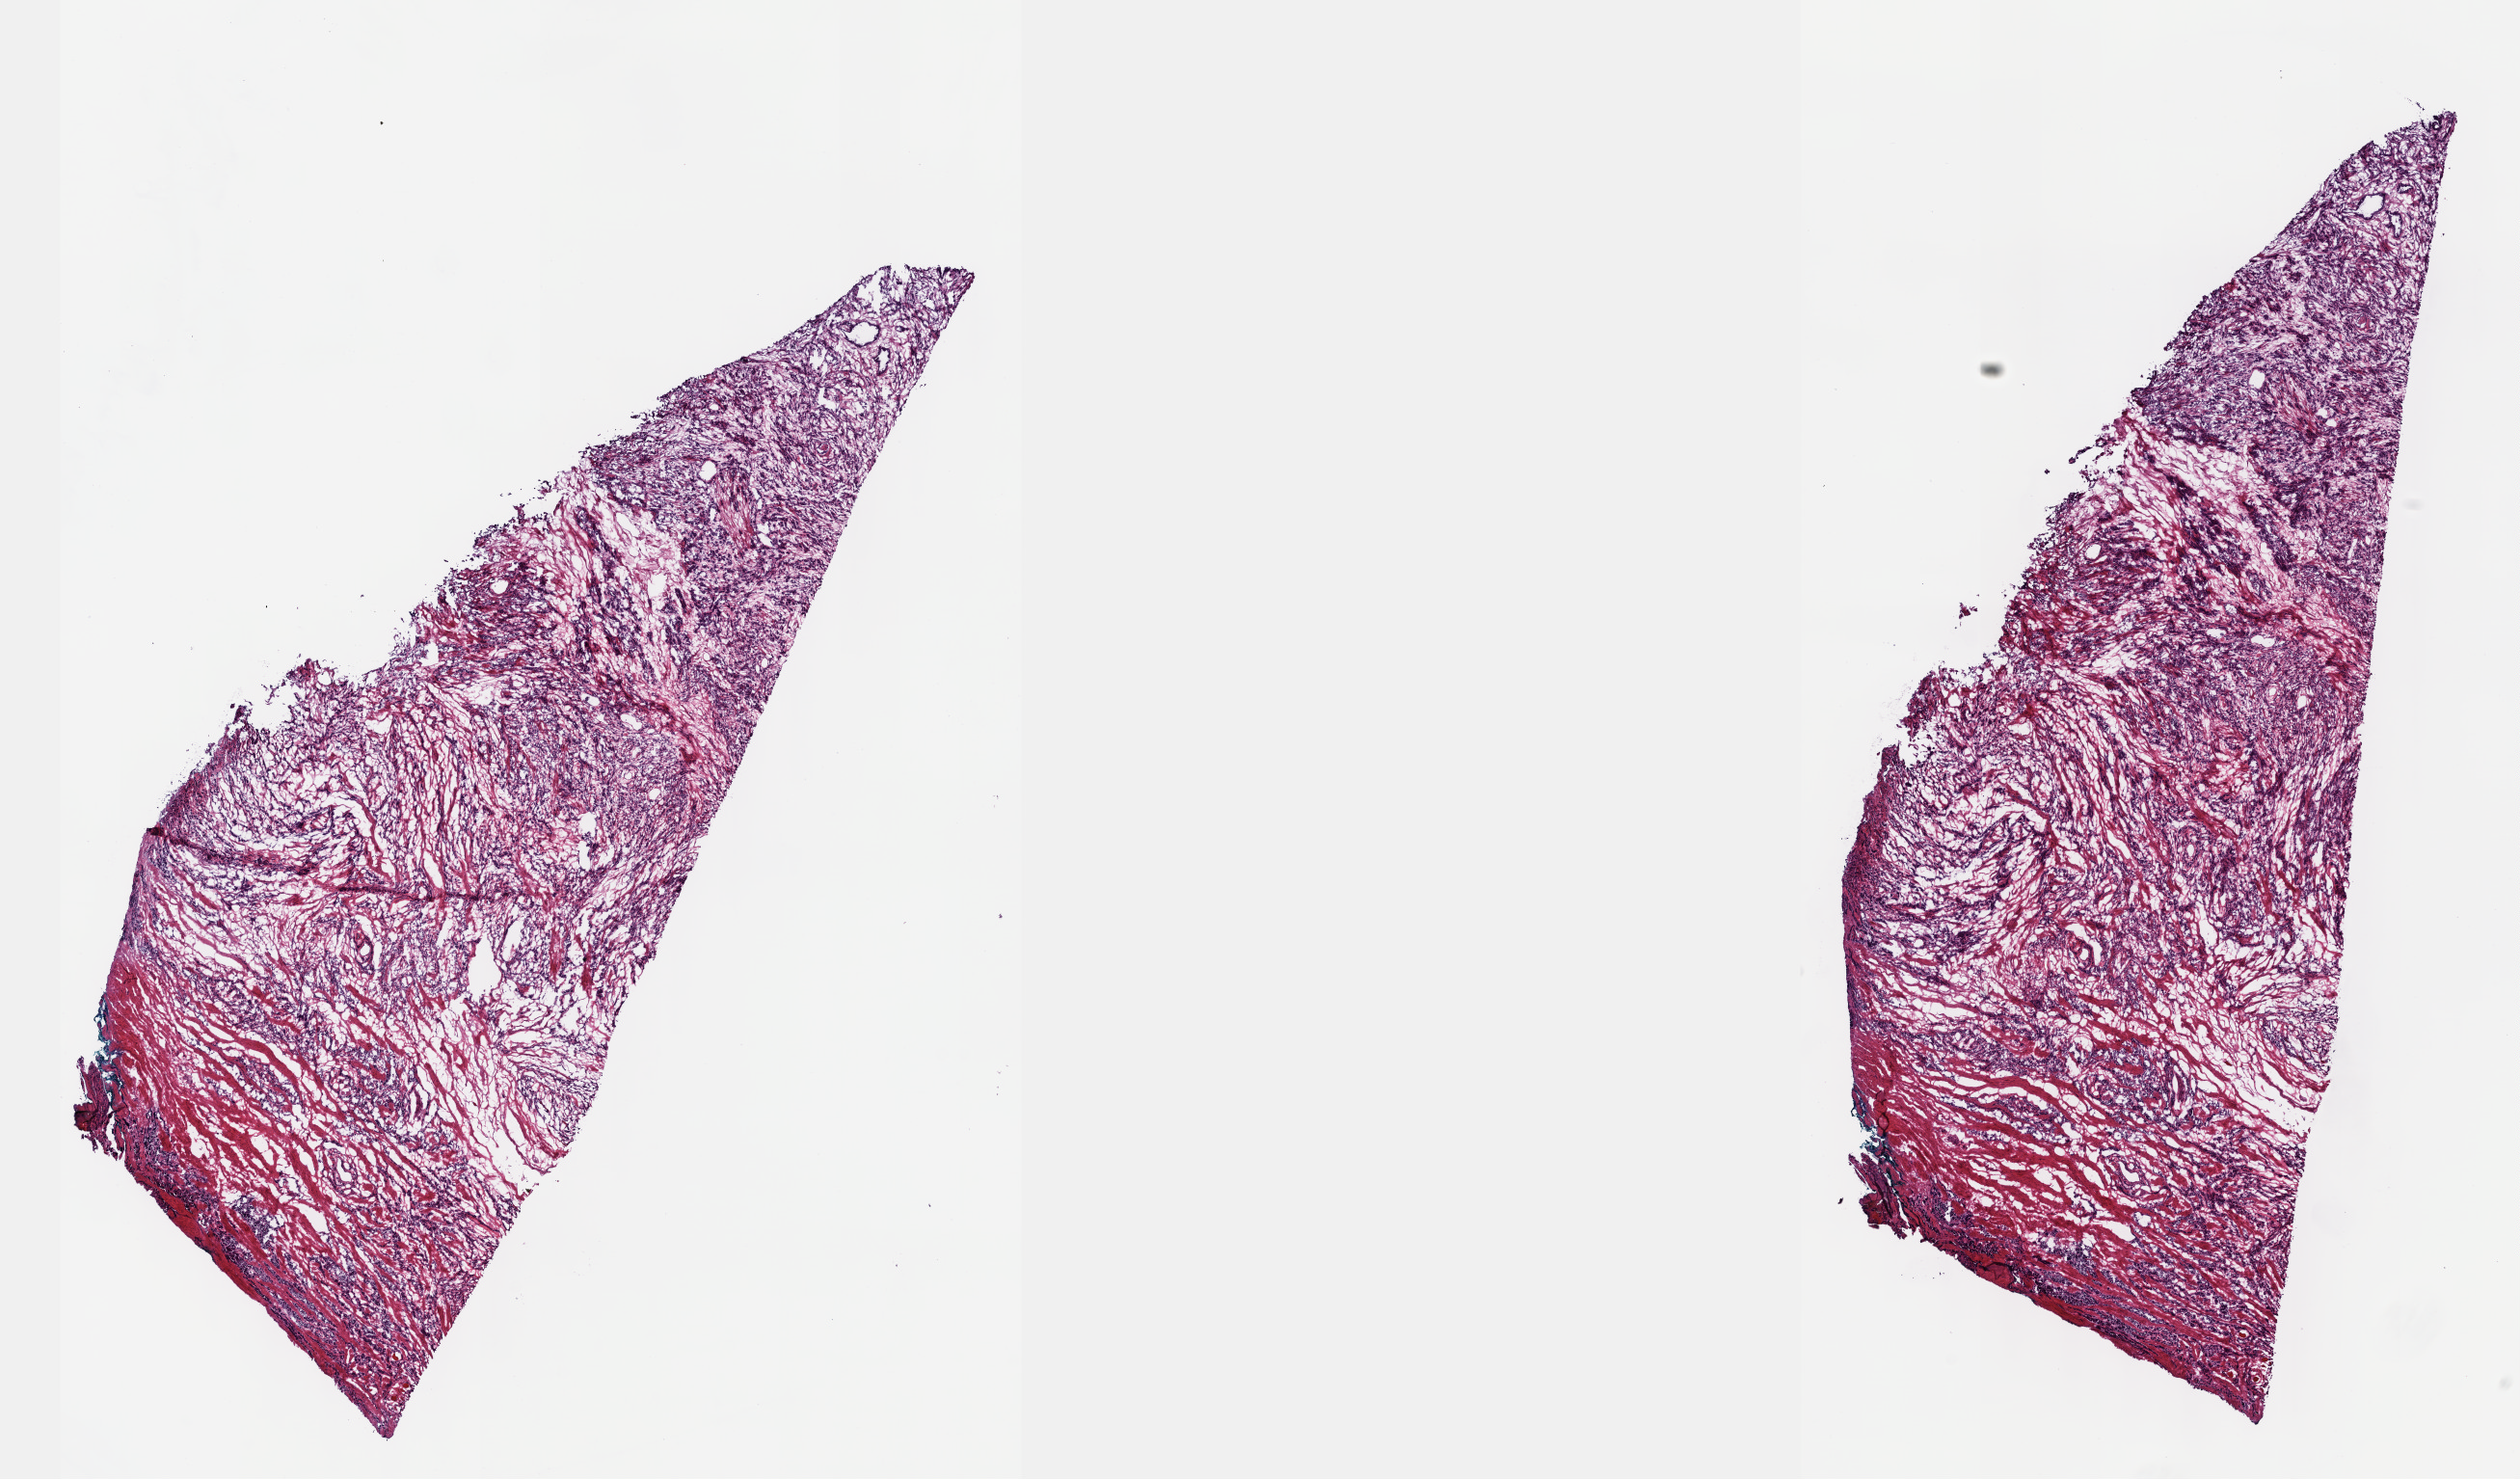
Digitized Hematoxylin and eosin (H&E) stained tissue section (whole slide), low-resolution overview of the scanned area, about 21.1 x 12.4 mm (from a 40x scan). Frozen section from the top of the tissue portion. Sample: primary tumour, prostate. Male patient; age at initial diagnosis 66 years. Gleason score: 9 (4+5). Slide review estimates, as recorded: tumour cells 50%, tumour nuclei 60%, normal cells 0%, stromal cells 50%, necrosis 0%. Infiltration values recorded for this section: lymphocyte infiltration 0%, monocyte infiltration 0%, neutrophil infiltration 0%.
Diagnosis: Adenocarcinoma, NOS. Laterality: bilateral.